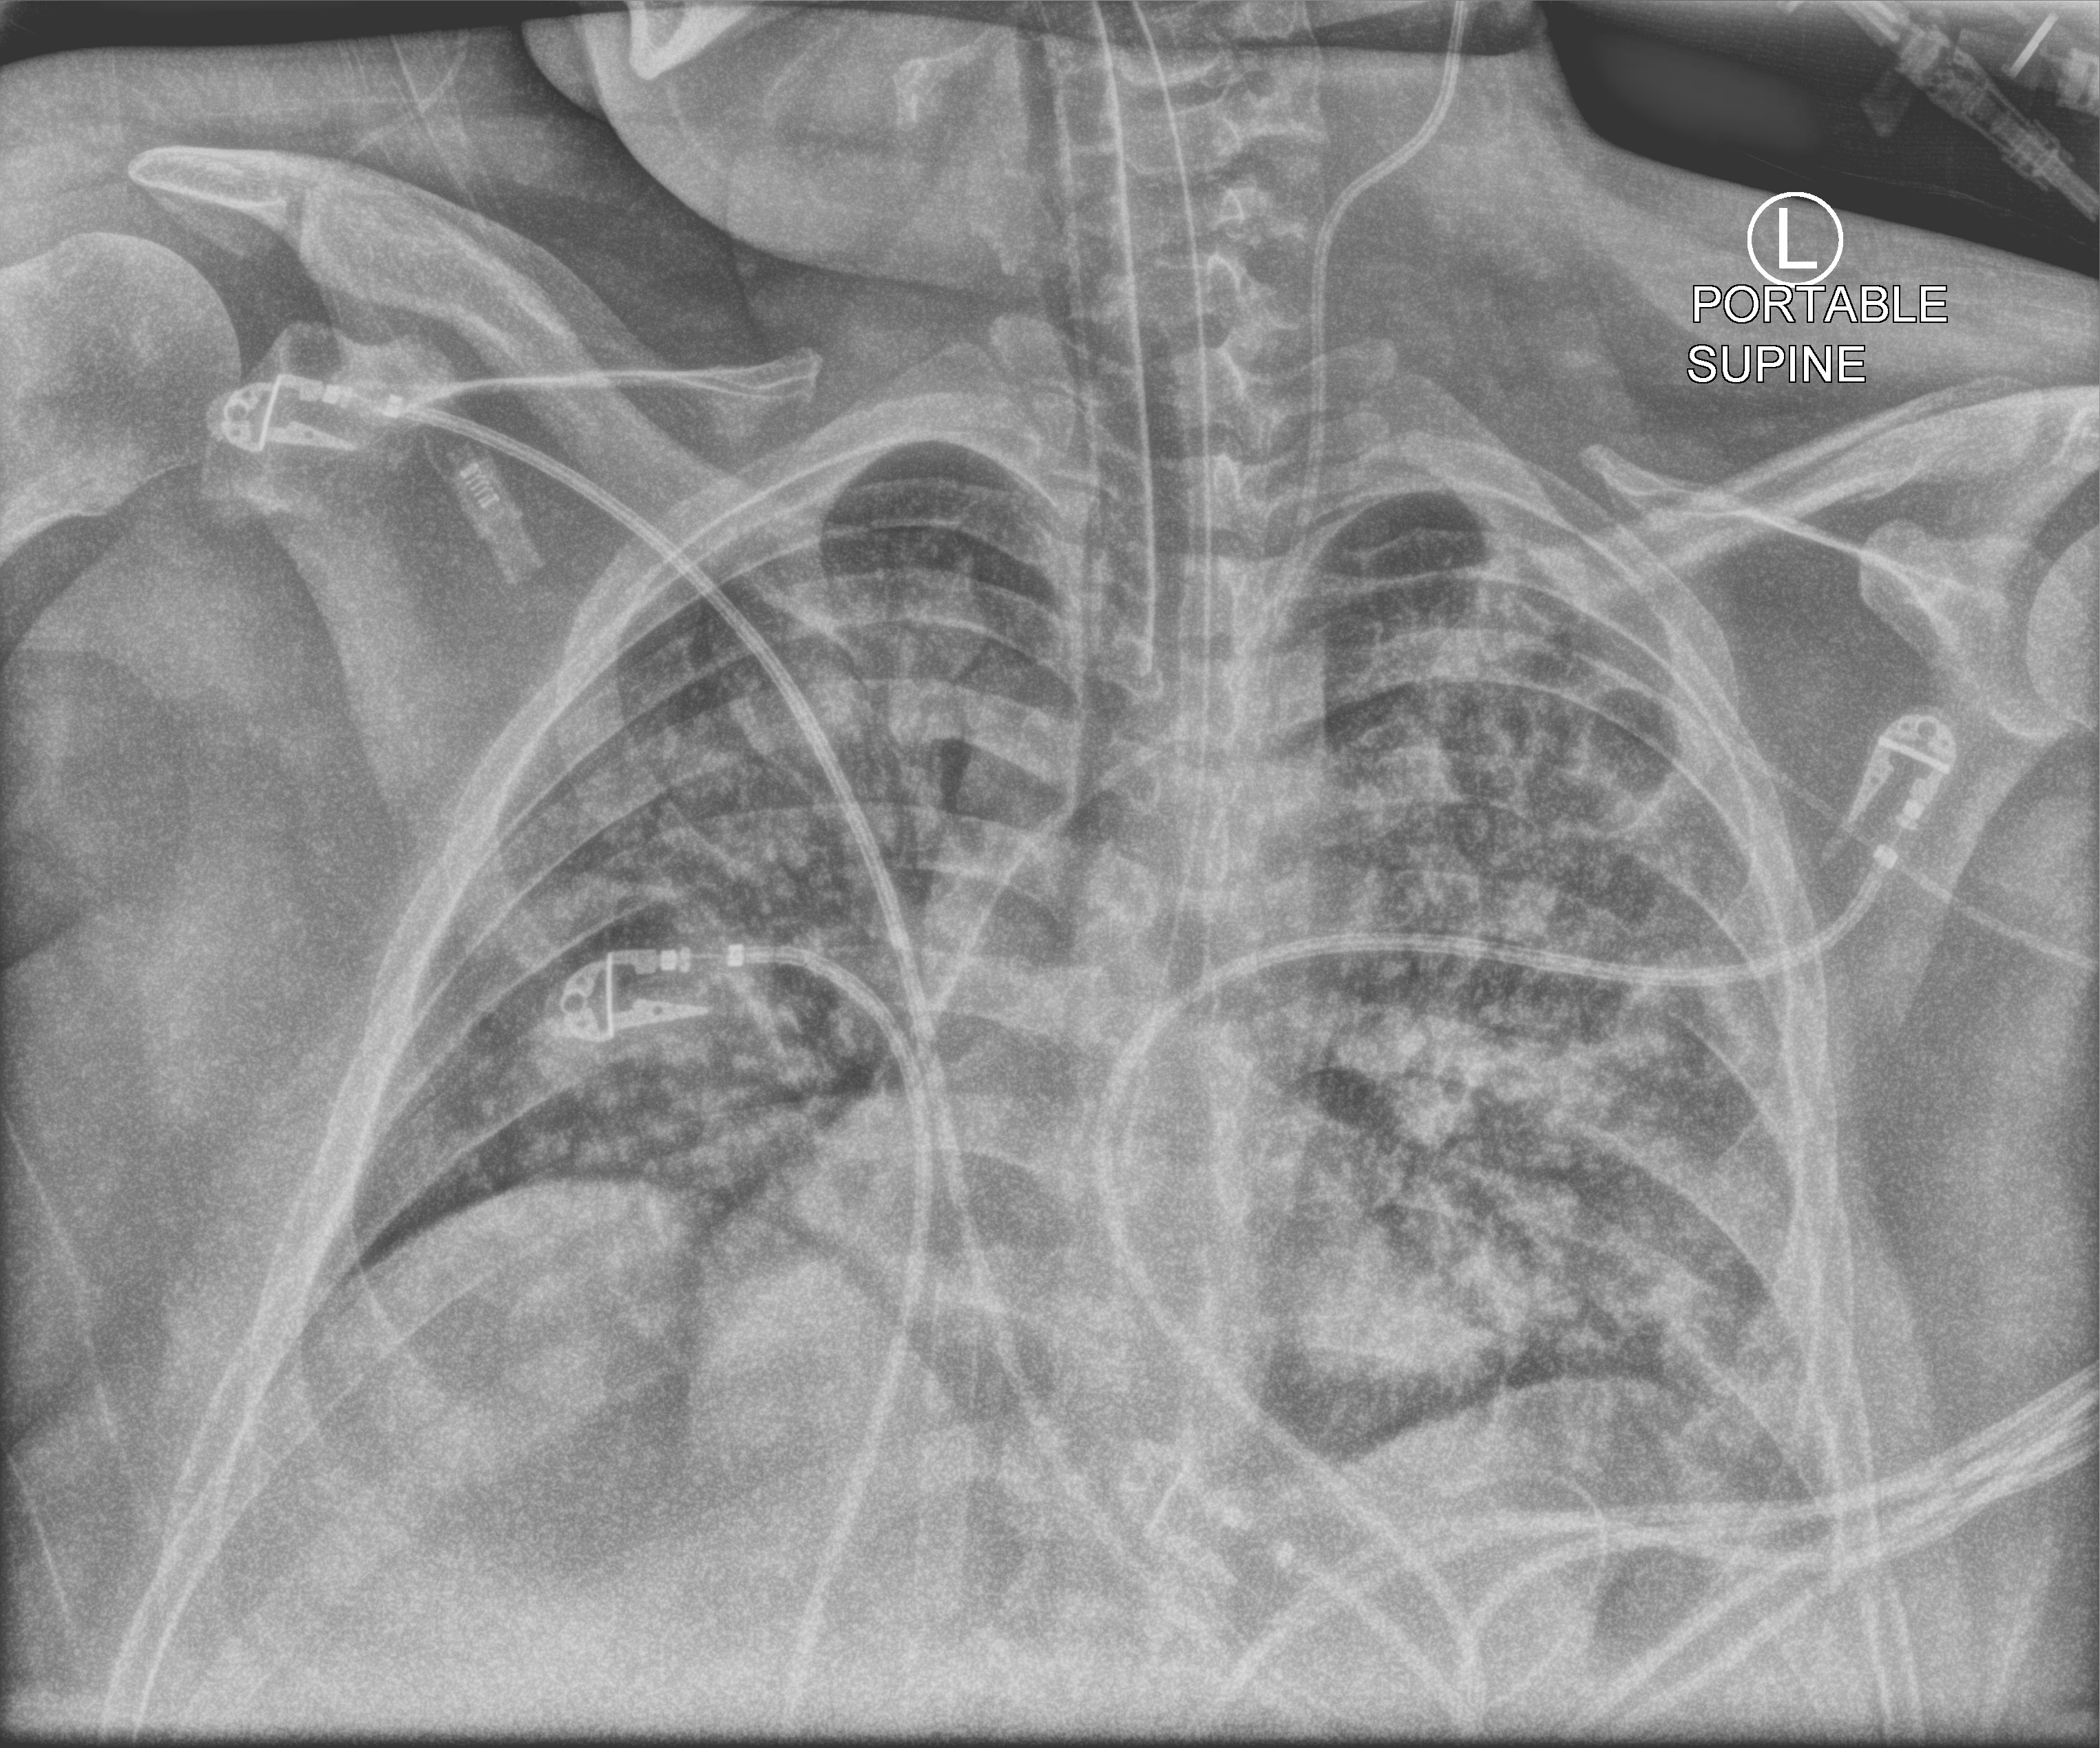
Chest X-ray (portable). Adult patient hospitalised with COVID-19, age 18–59 years.
Hospital-stay facts (about this admission, not read from this image; timing relative to this image not recorded): admitted to intensive care during this hospital stay: yes; diabetes (admission record): no; mechanically ventilated during this hospital stay: yes.